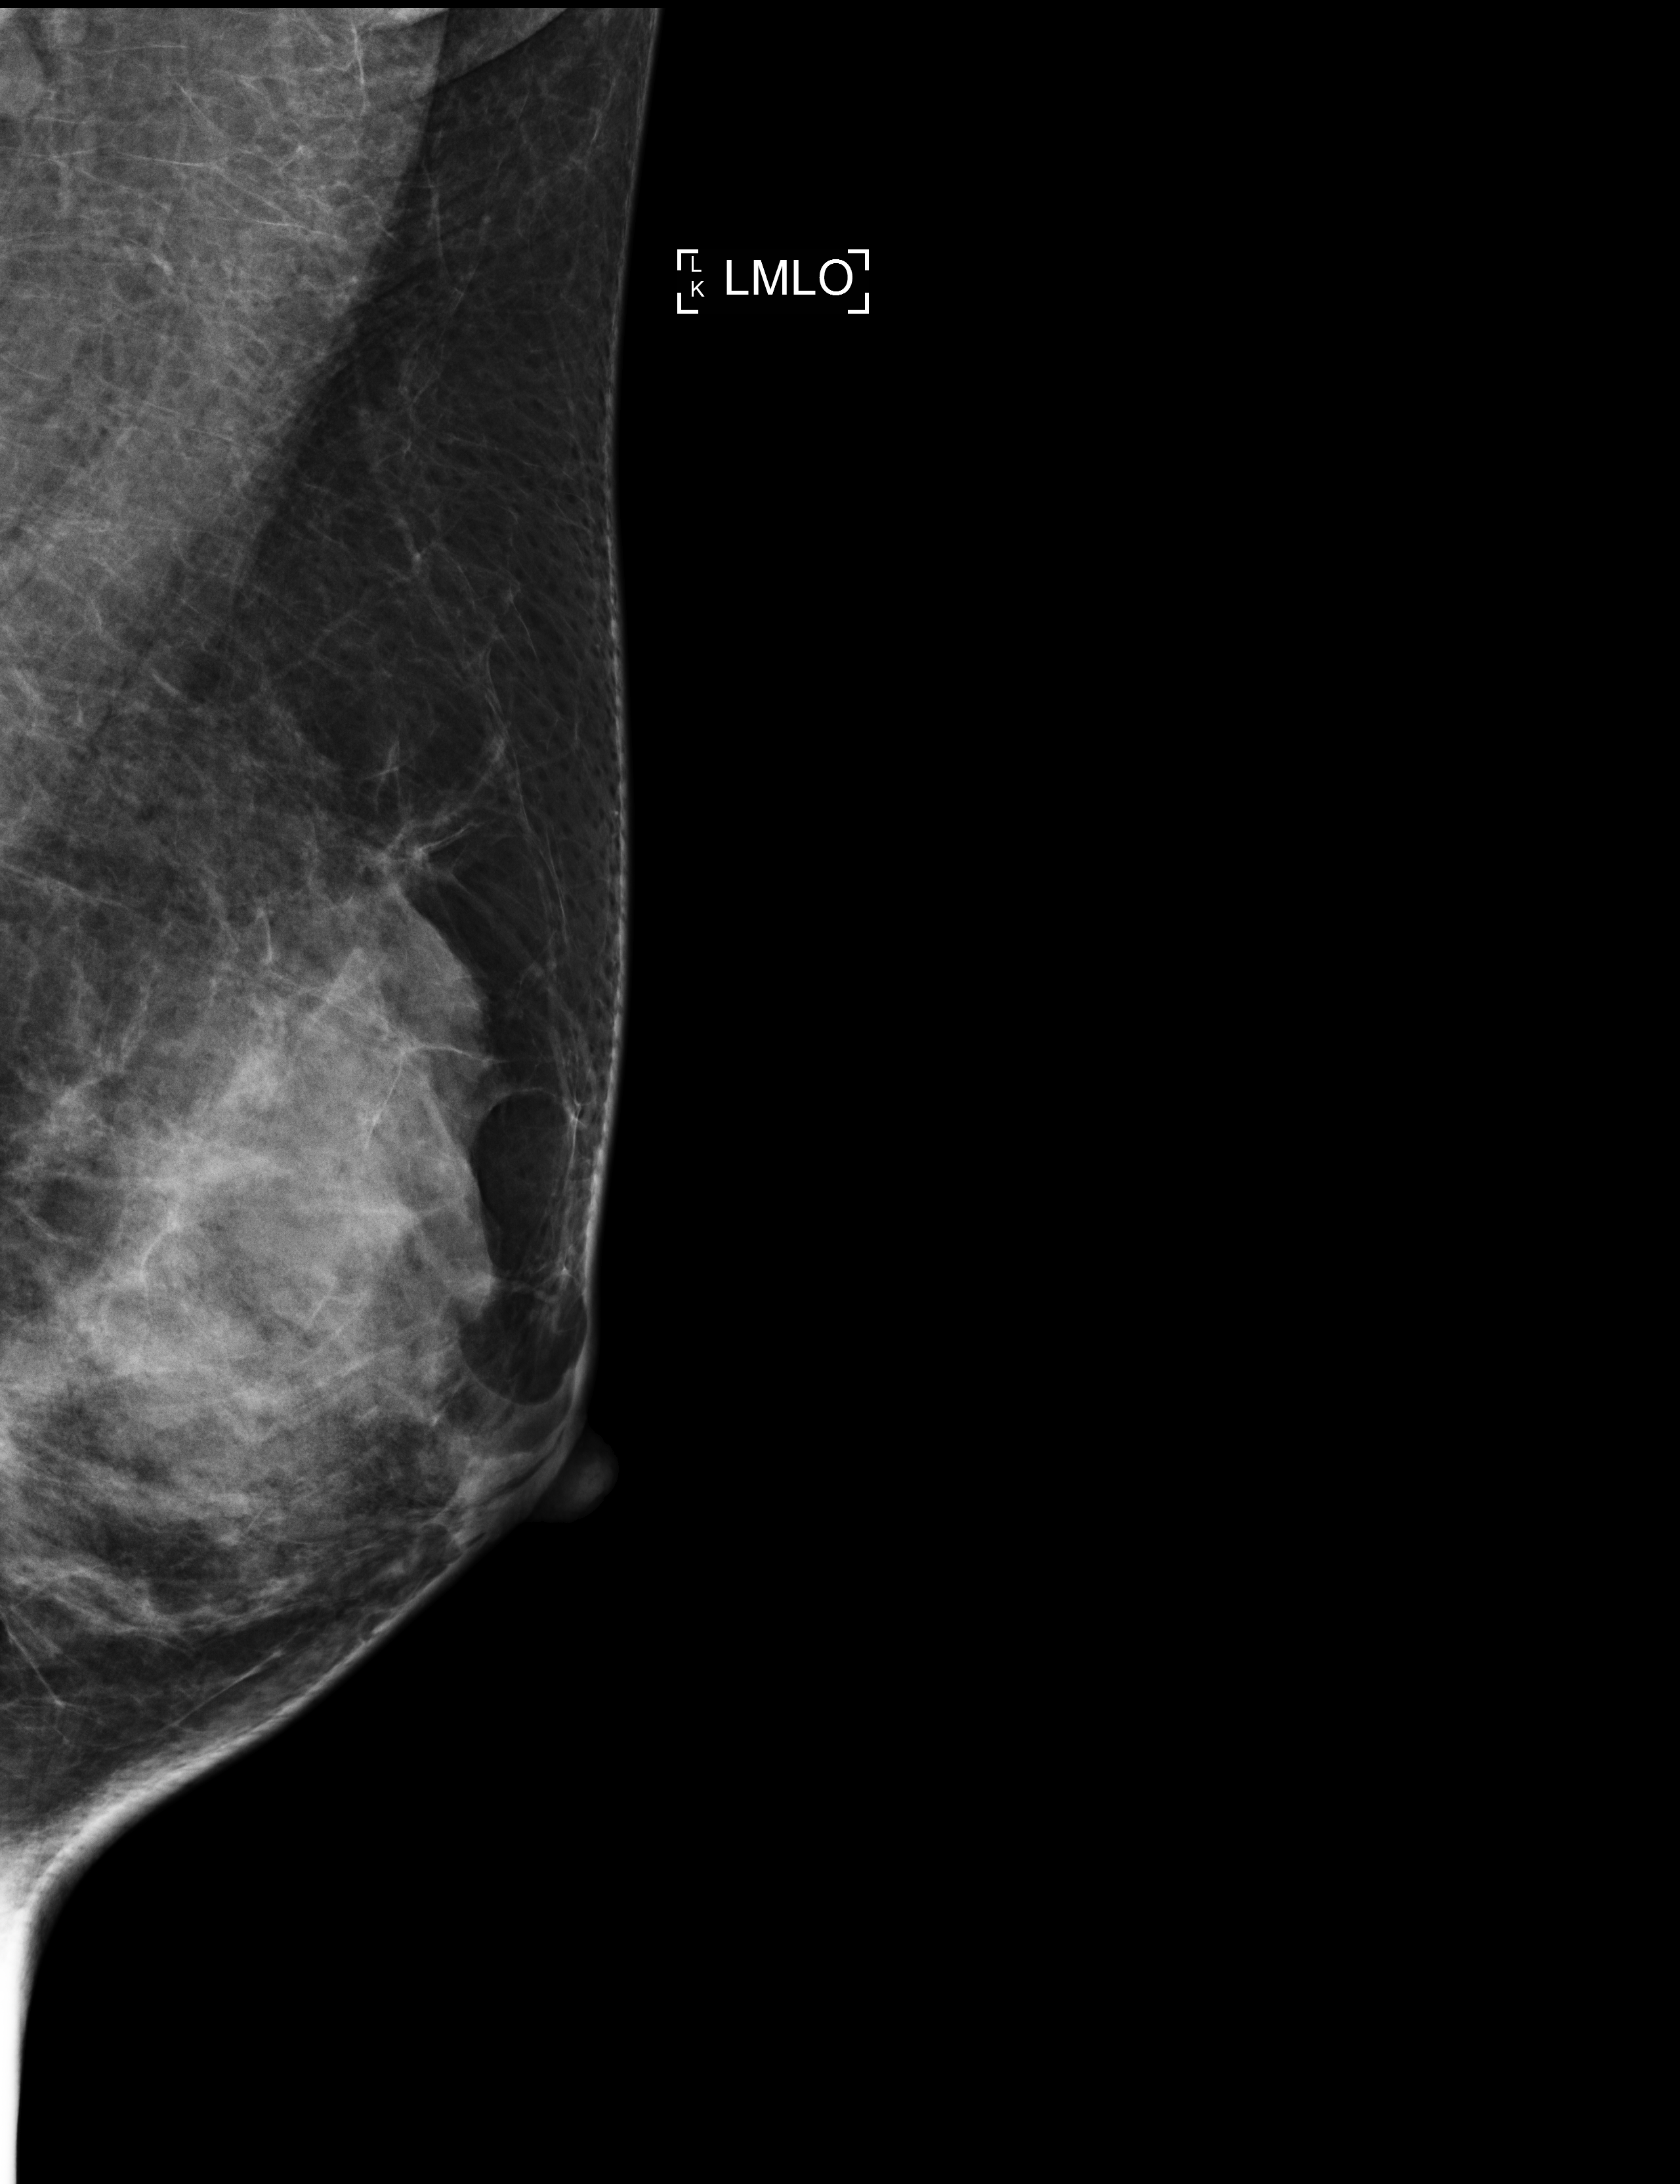
Screening examination; compressed breast thickness 52 mm. Patient aged 44 years (female).
Image type: full-field digital mammogram. Breast: left. Projection: medio-lateral oblique projection.